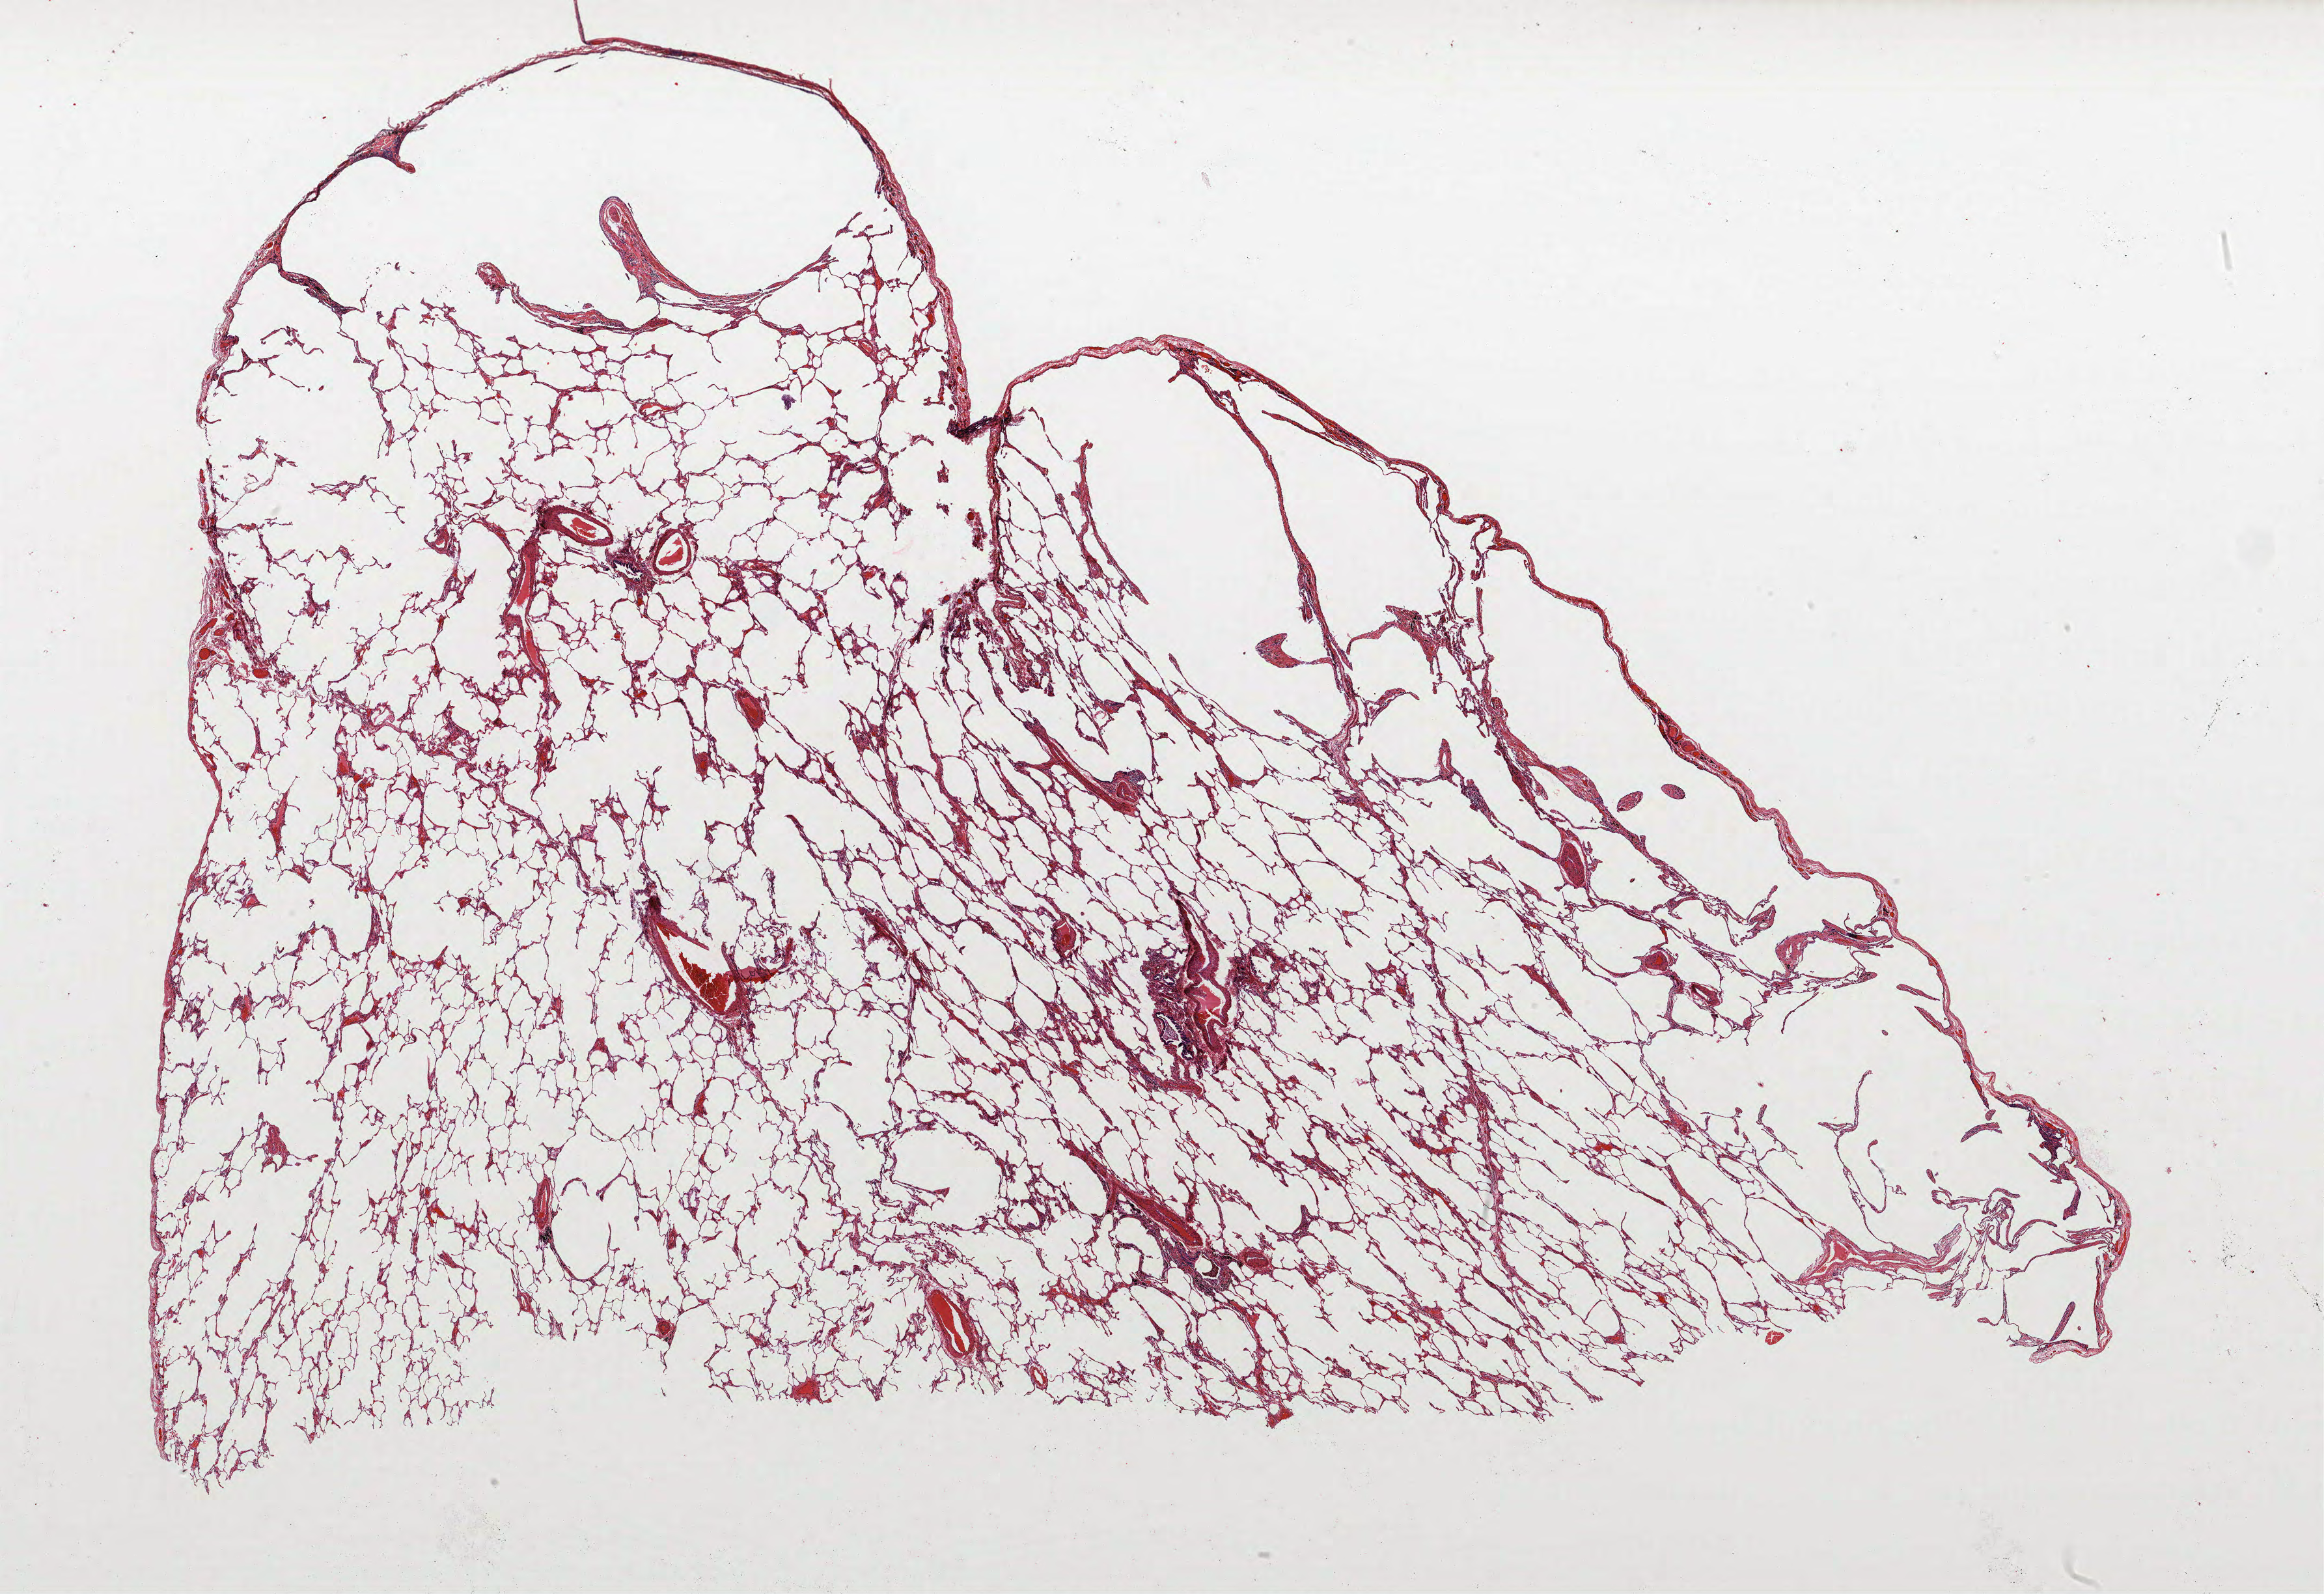
Whole-slide histology image, H&E-stained — whole scanned area (about 28.6 x 19.6 mm, from a 40x scan) shown as a low-resolution overview, FFPE section, lung. Male, age 68 at enrolment. Grade: moderately differentiated (G2).
- participant's lung-cancer diagnosis: Squamous cell carcinoma, NOS
- tumour size (pathology): 25 mm
- stage (AJCC 6th edition): IIA
- primary tumour location (clinical record): left upper lobe